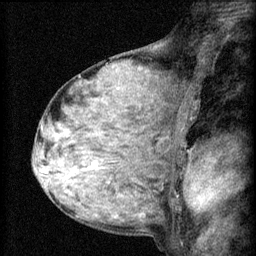
Breast MRI (dynamic contrast-enhanced), one sagittal slice. 3 images stored at this slice position (order not interpretable as contrast timing). 1.5 T. TE 4.2 ms, TR 8.2 ms. 256 × 256 image matrix. Female patient, age 48 years.
Annotated regions visible in this slice (semi-automatic segmentation, software-assisted and operator-edited):
- analysis volume of interest (the breast-tissue region the enhancement analysis was run in; not a lesion): box from (x=54, y=138) to (x=133, y=191) px
- tumour enhancement mask (voxels above the 70 % enhancement threshold inside the analysis volume of interest): (x=88, y=162)–(x=97, y=169)